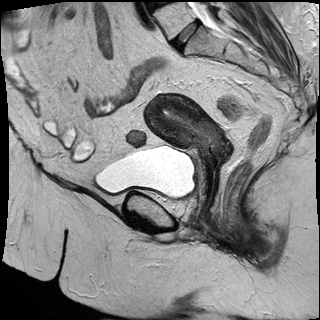
Pelvic MRI for cervical cancer, one sagittal slice. T2-weighted. 1.5 T. TE 87 ms, TR 3063.4 ms. 4 mm slice thickness. 320 × 320 image matrix, field of view 280 × 280 mm. Patient: female, 53 years.
Outlined on this slice (expert manual segmentation):
- uterus and cervix: bounding box (x1, y1, x2, y2) in pixels: (144, 93, 225, 169)